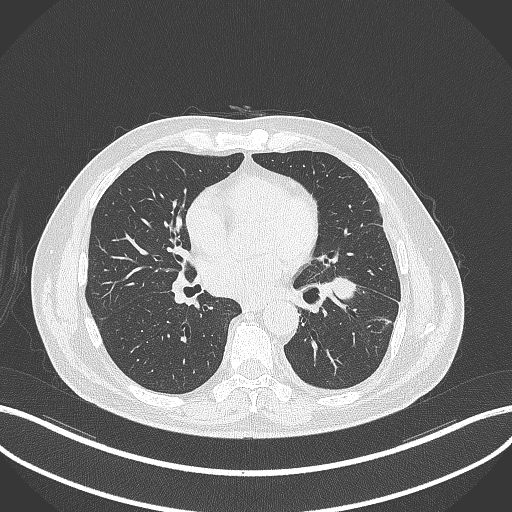
Chest CT, one axial slice. Position 170 of 230 along the scan axis. 120 kVp. Lung window (W 1500 / L -600 HU). 1 mm slice thickness. 512 × 512 image matrix. Patient: male, 68 years. From the clinical record (not read from this slice): clinical TNM (as recorded): T2b N0 M0.
Structures marked on this image (rectangle marked by the reading radiologist):
- lung tumour (recorded histology: squamous cell carcinoma): box from (x=326, y=273) to (x=362, y=303) px